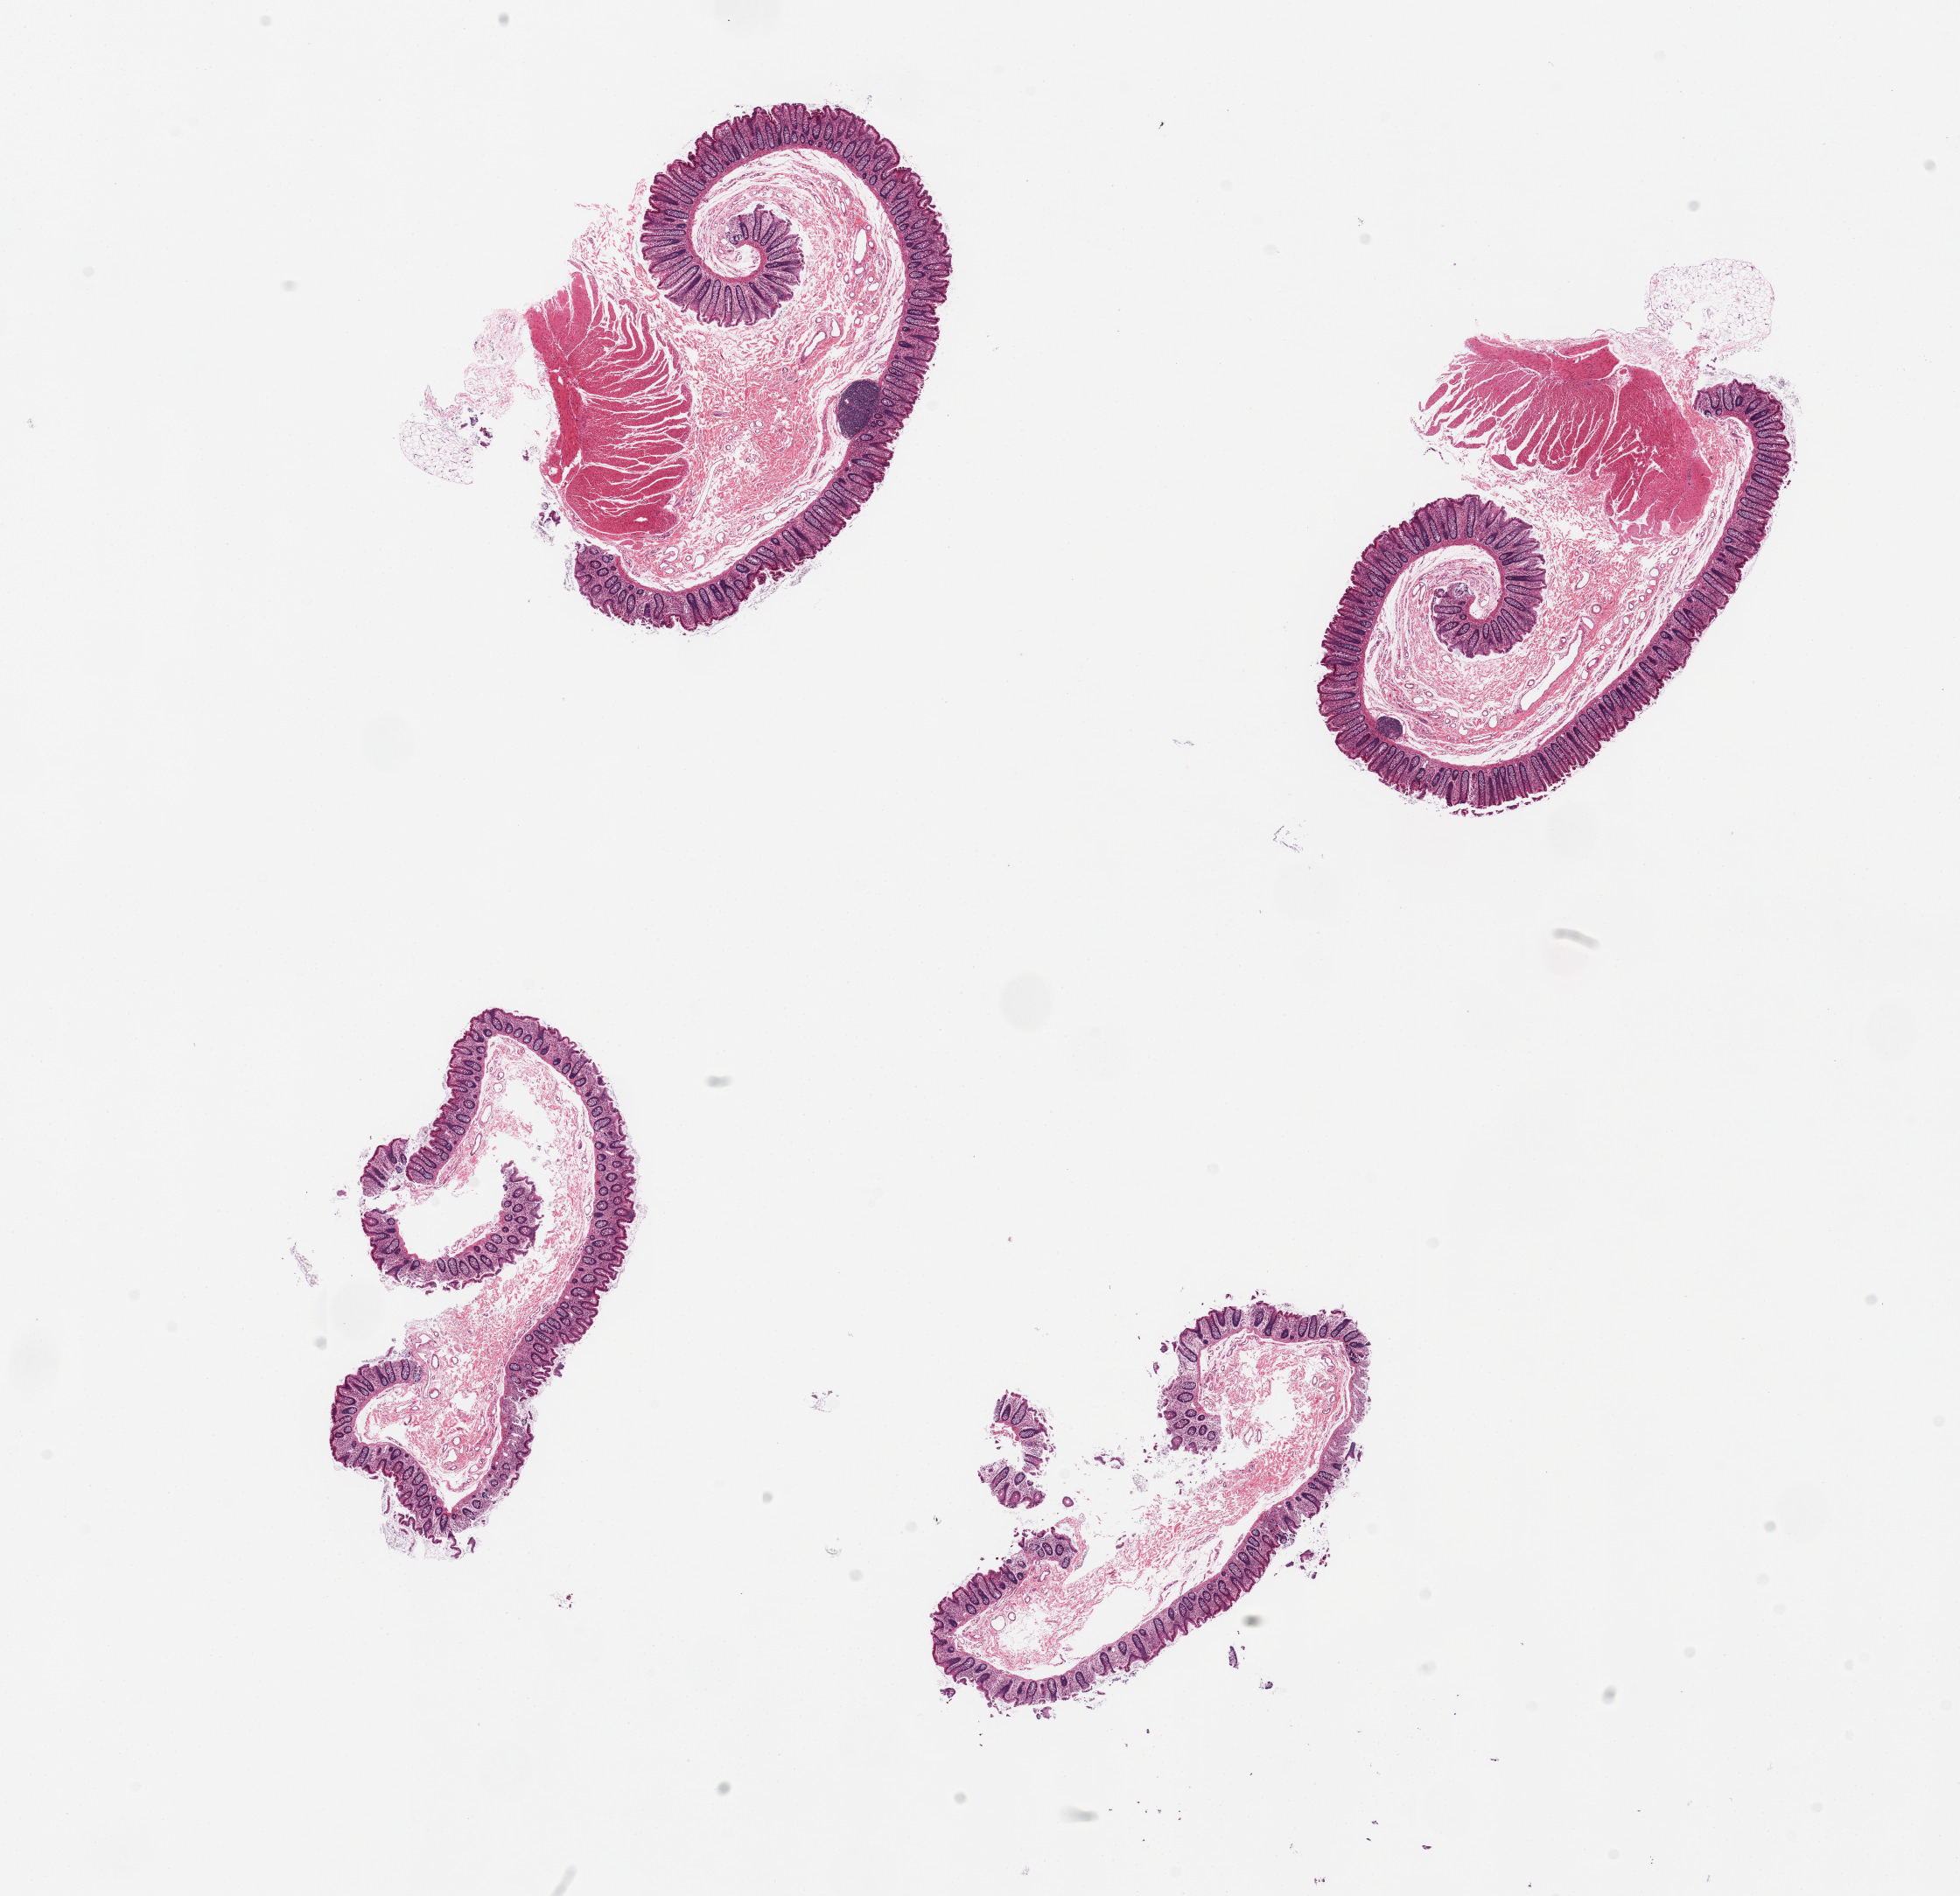
Whole-slide image, hematoxylin and eosin (H&E) stain, a low-resolution overview of the entire scanned area, about 17.7 x 17.1 mm (slide scanned at 20x), PAXgene-fixed, paraffin-embedded tissue, sampled site (target tissue): transverse colon, donor tissue sample. Donor sex: female.
Reviewer comment on this tissue sample: 4 pieces, 2 are mucosa and submucosa, two include mucosa and muscularis.